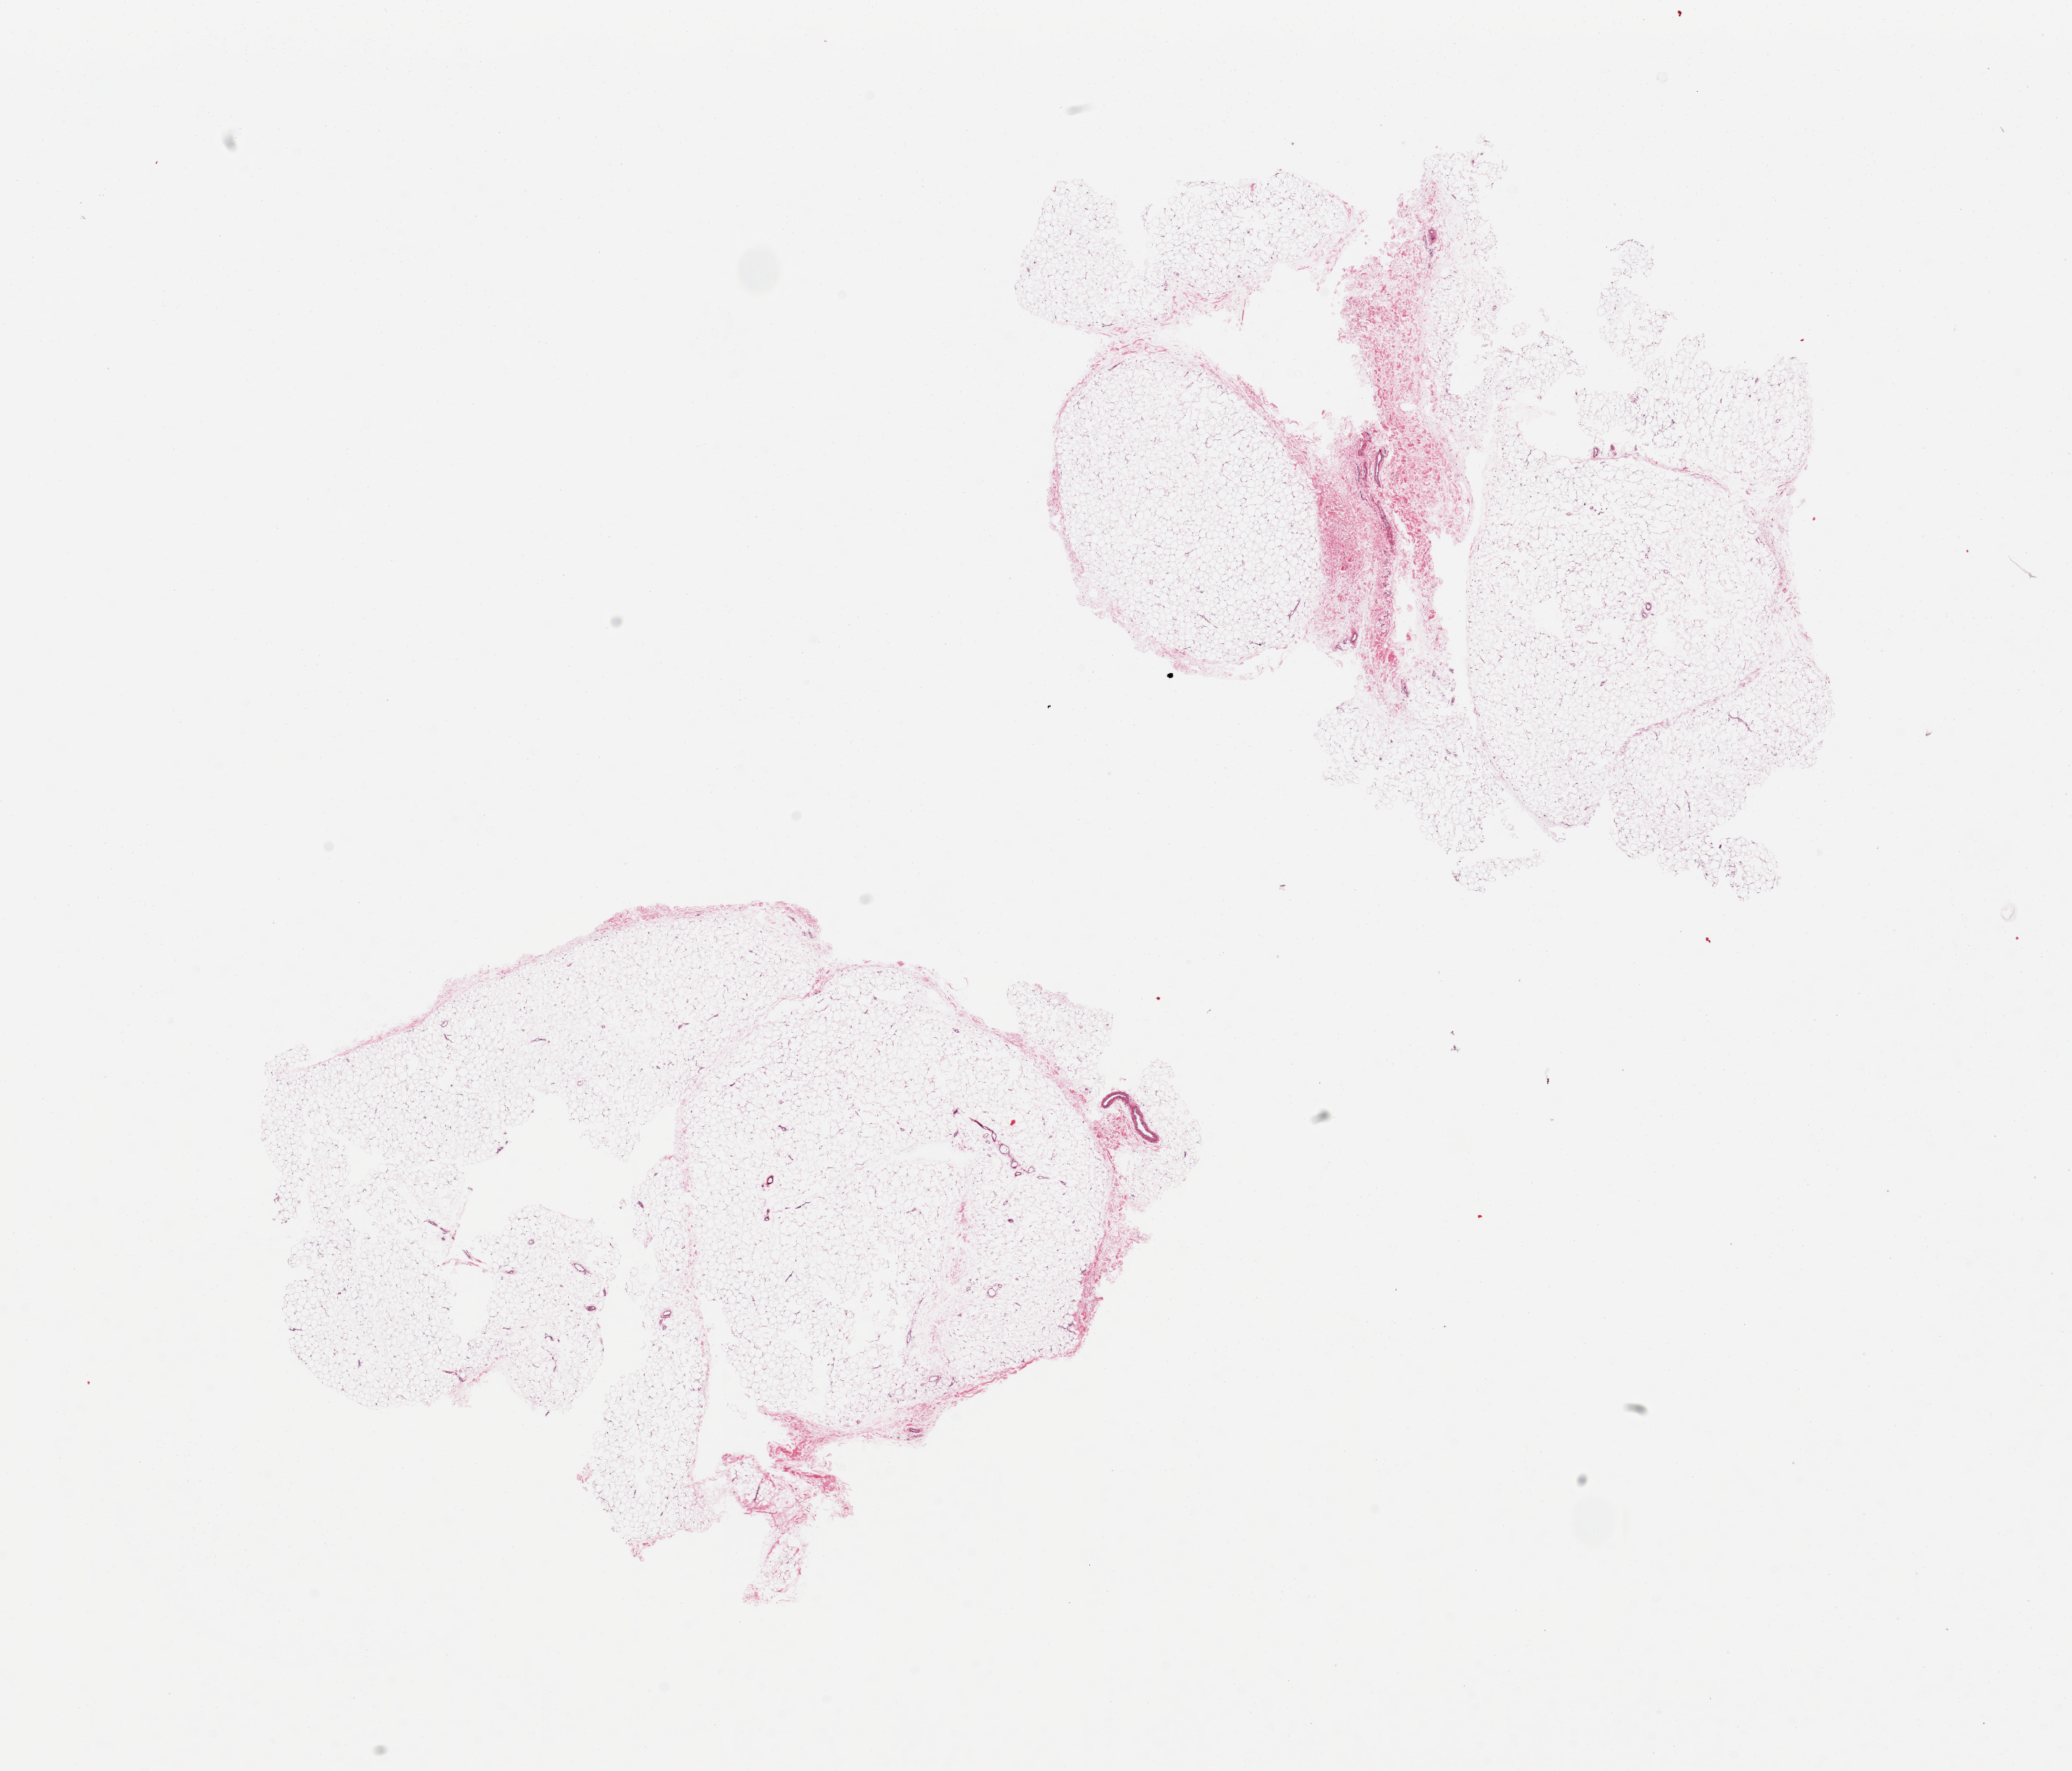
H&E whole-slide image, a low-resolution overview of the entire scanned area, about 22.6 x 19.4 mm (from a 20x scan); PAXgene-fixed, paraffin-embedded tissue; section of adipose tissue (target tissue); tissue donor sample. Donor: female.
- review note (as recorded): 2 pieces, defects in section (? poor fixation), one is about 15% fibrous tissue